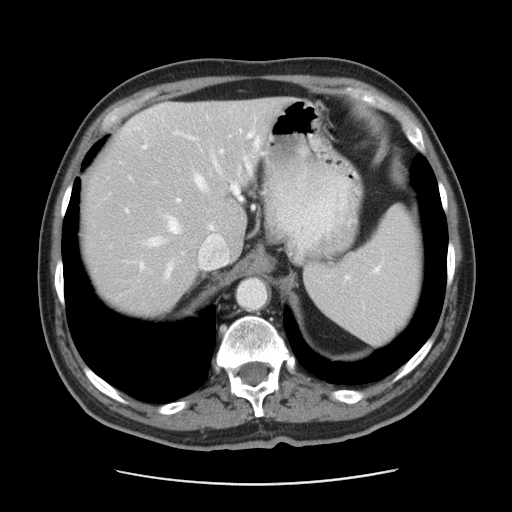
Contrast-enhanced abdominal CT, one axial slice; position 33 of 42 along the scan axis; intravenous contrast given; soft-tissue window (W 400 / L 40 HU); 5 mm slice thickness; 512 × 512 image matrix, field of view 370 × 370 mm. Male patient, age 73 years. Case-level facts recorded for this patient, not image findings: diagnosis: colorectal cancer liver metastases, imaged before liver resection; multiple liver metastases: yes; largest metastasis: 0.5 cm; disease in both lobes: no.
Annotated regions visible in this slice (manually delineated by an expert):
- hepatic veins: bounding box (x1, y1, x2, y2) in pixels: (136, 141, 258, 281)
- liver: (82, 99, 284, 313)
- planned liver remnant (the part of the liver to remain after resection): (119, 99, 285, 254)
- portal vein (with intrahepatic branches): (126, 129, 259, 267)